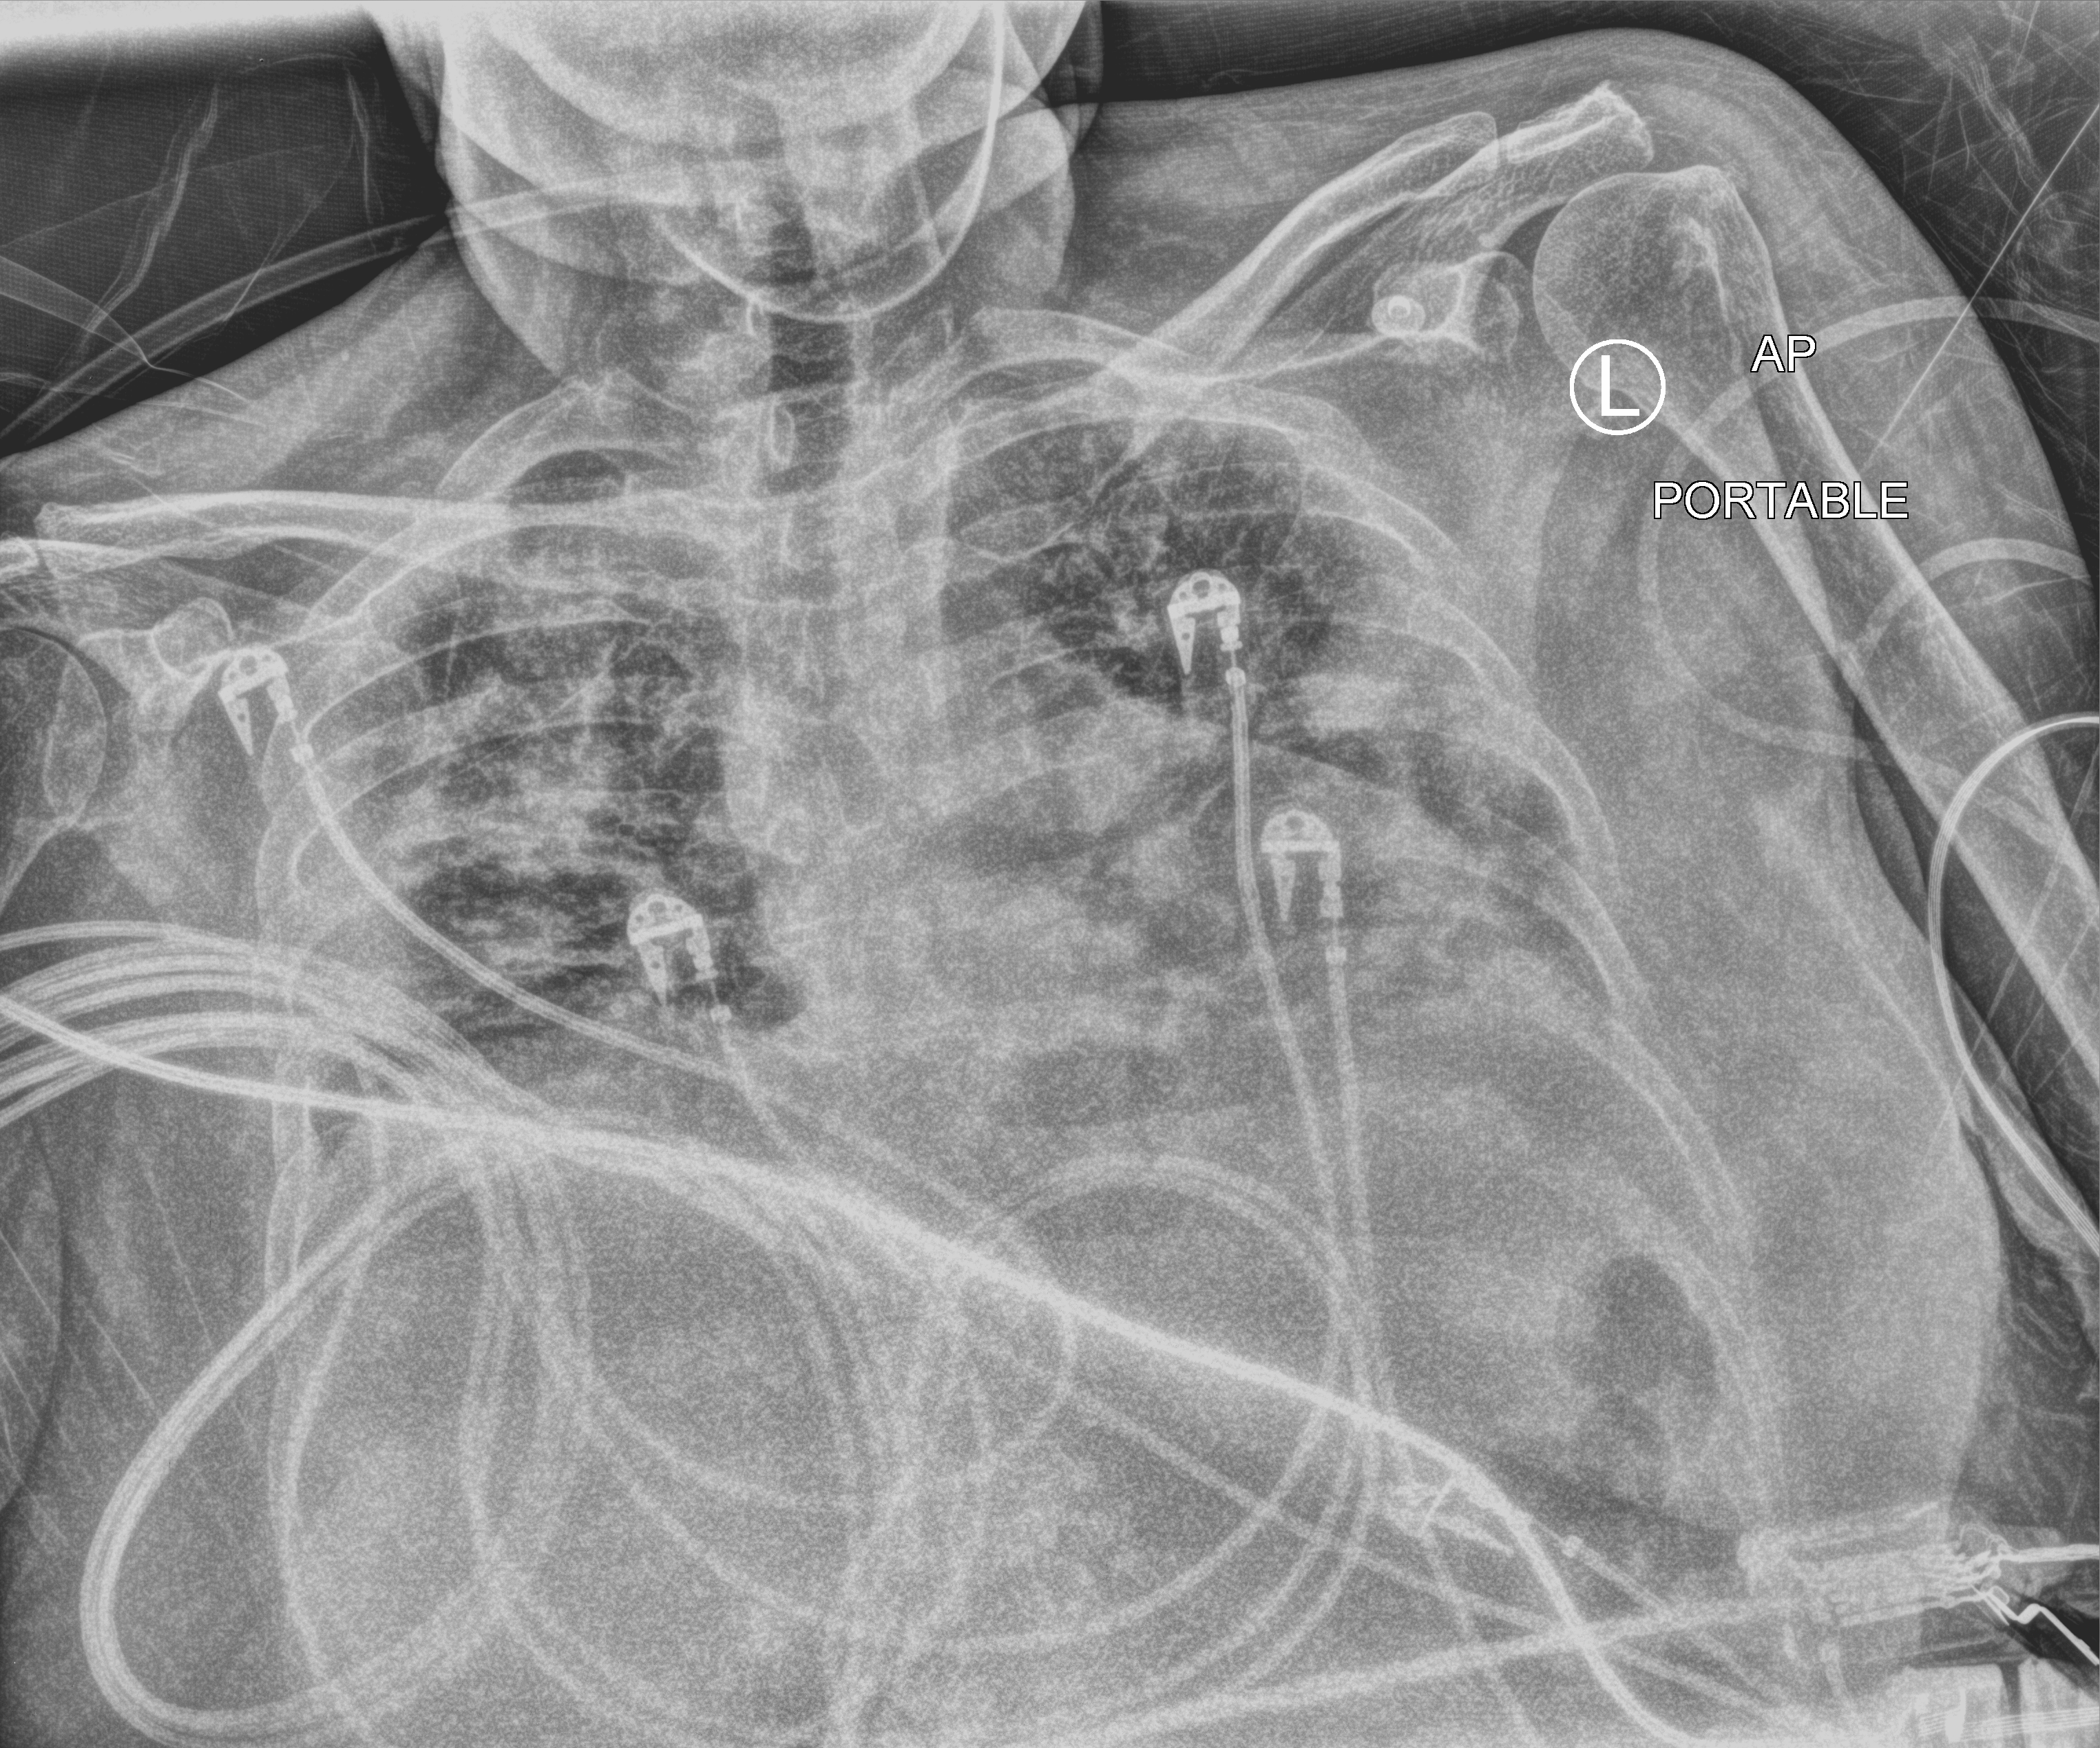
Portable chest radiograph, anteroposterior (AP) projection. Female patient hospitalised with COVID-19, age 18–59 years.
Admission-level facts for this patient (not findings on this image; timing relative to this image not recorded):
- hypertension (admission record): yes